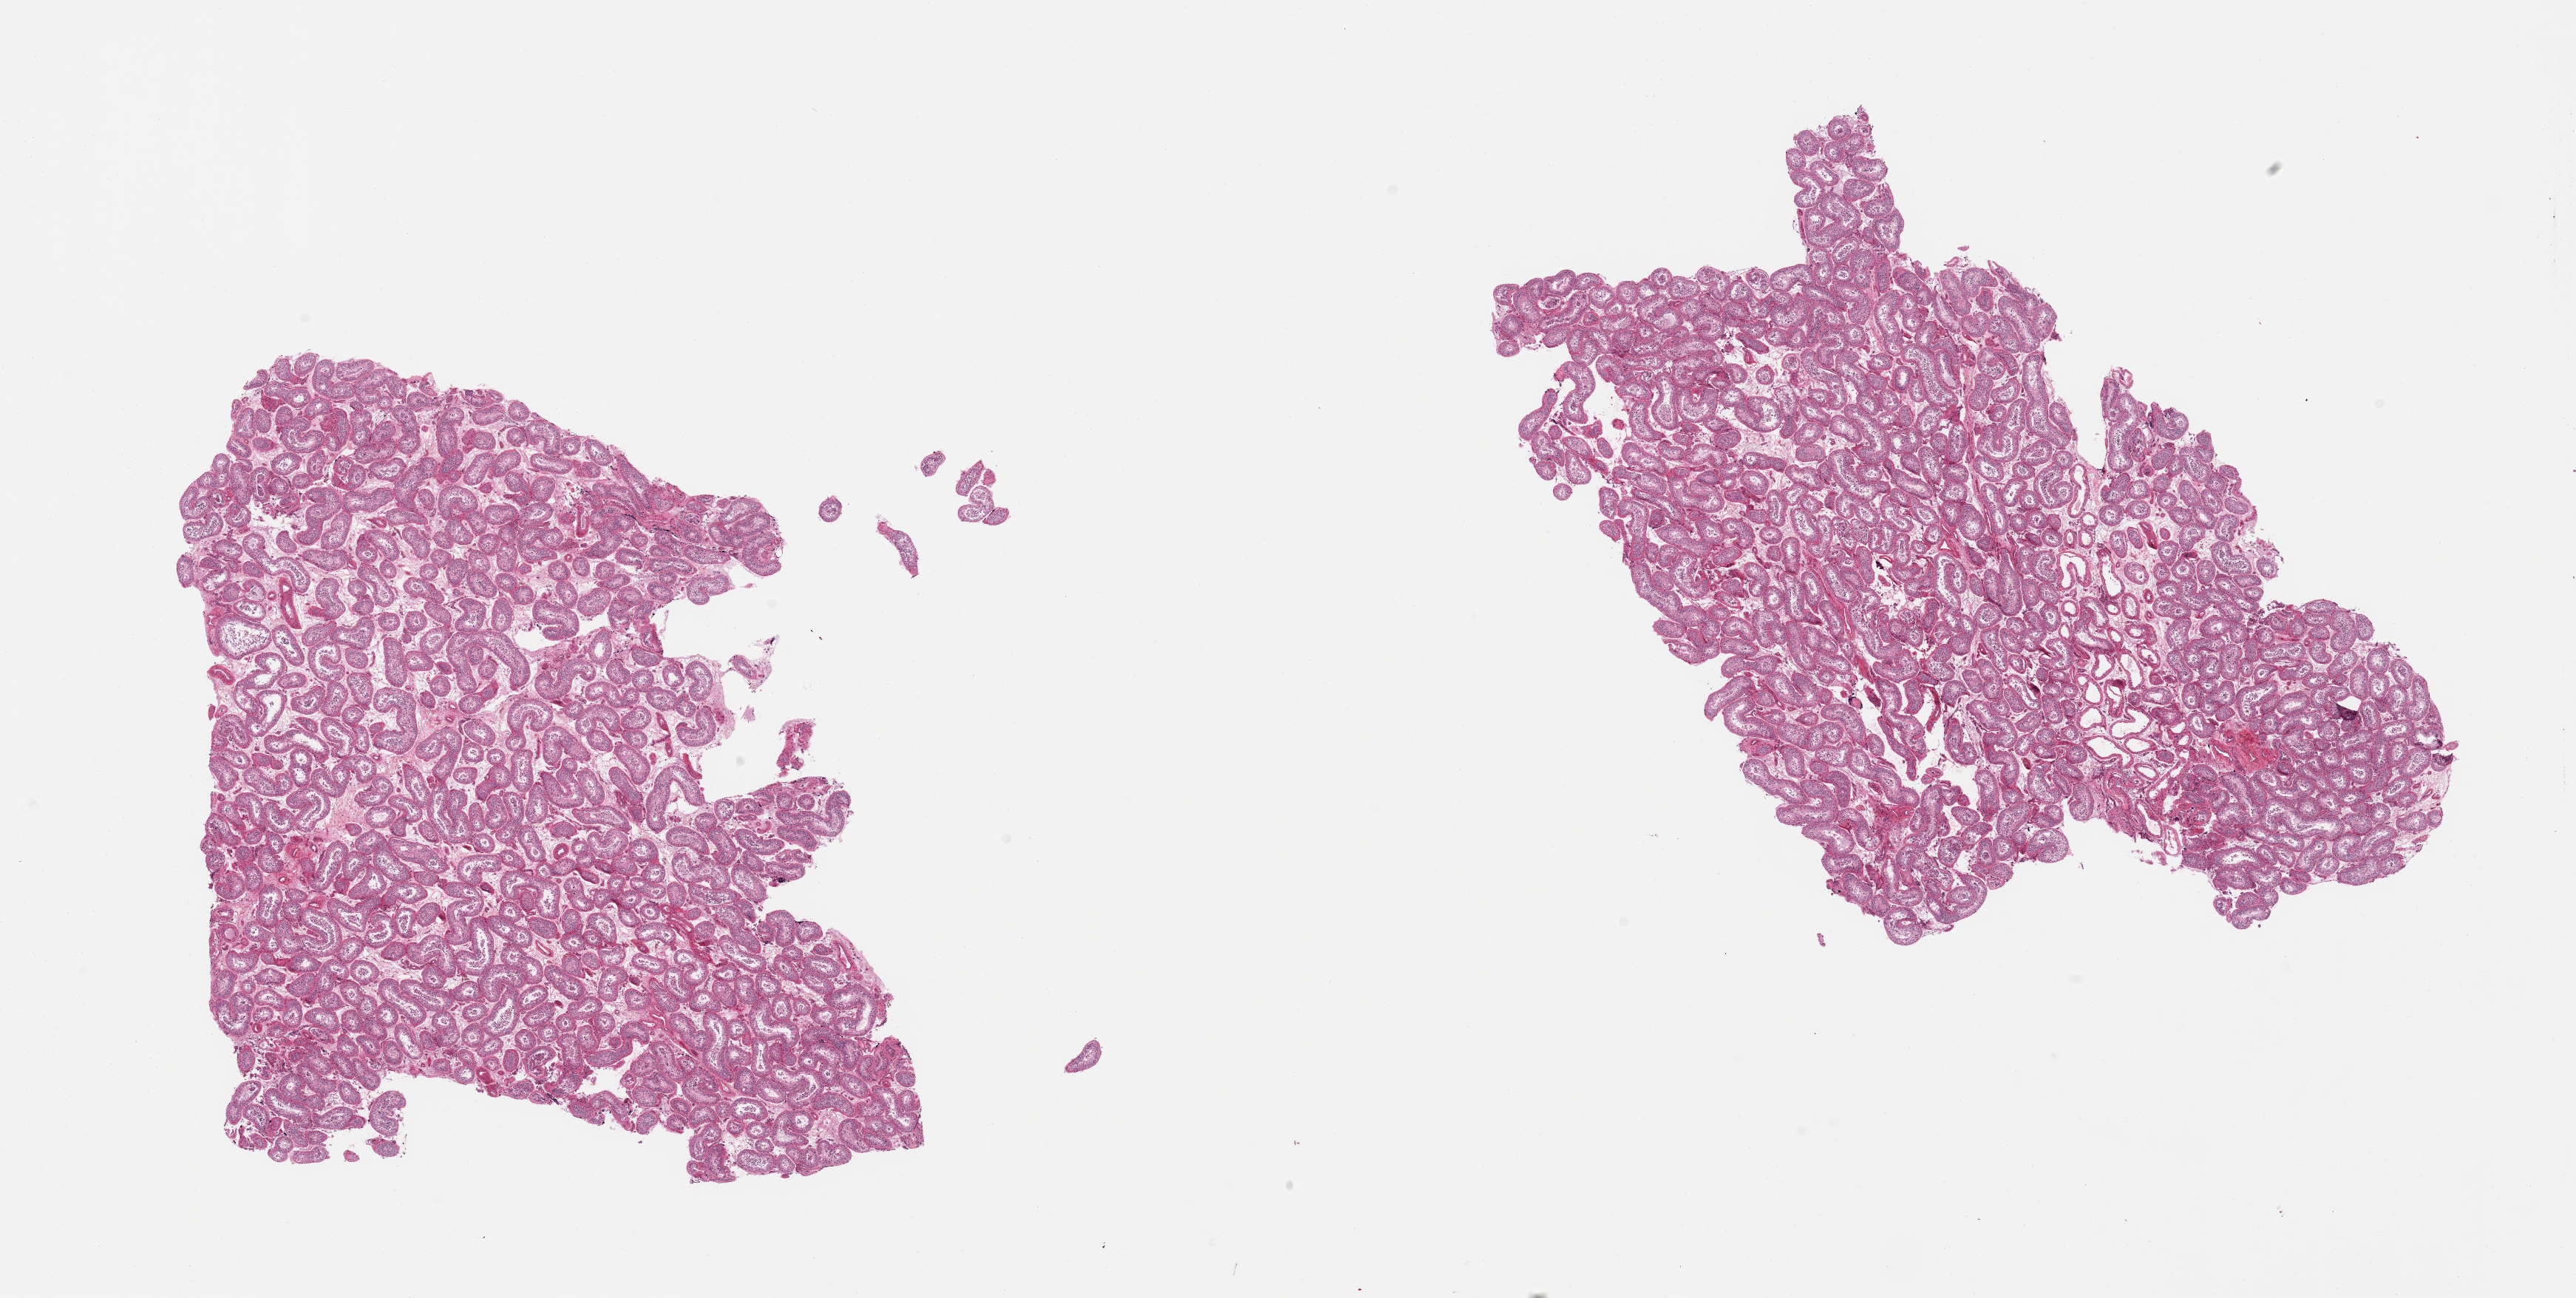
Digitized H&E-stained section, whole scanned area (about 27.6 x 13.9 mm) shown as a low-resolution overview, PAXgene-fixed paraffin-embedded (PFPE) section, section of testis (target tissue), tissue donor sample. Donor: male.
Reviewer comment on this tissue sample: 2 pieces, well preserved. Spermatogenesis is present but appears reduced.